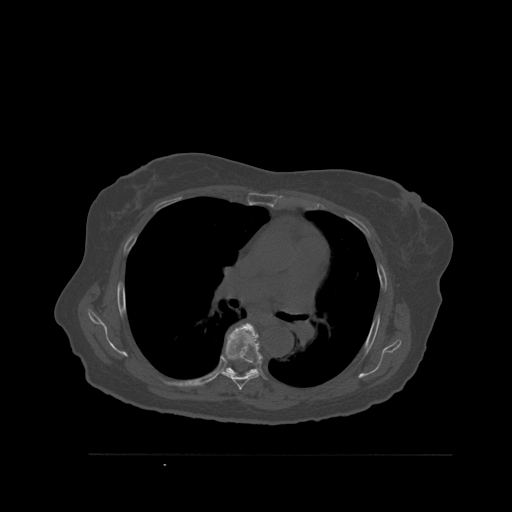
CT including the spine, one axial slice. Position 376 of 527 along the scan axis. Bone window (W 1800 / L 400 HU). 1.5 mm slice thickness. 512 × 512 image matrix, field of view 470 × 470 mm. Female patient, age 73 years. From the clinical record (not read from this slice): primary cancer: breast; vertebrae with lytic lesions (as recorded): L2.
Outlined on this slice (semi-automatically segmented with operator editing):
- T6 vertebra: bounding box <222,322,263,391> (left, top, right, bottom; pixels)
- T7 vertebra: <226,367,258,376>